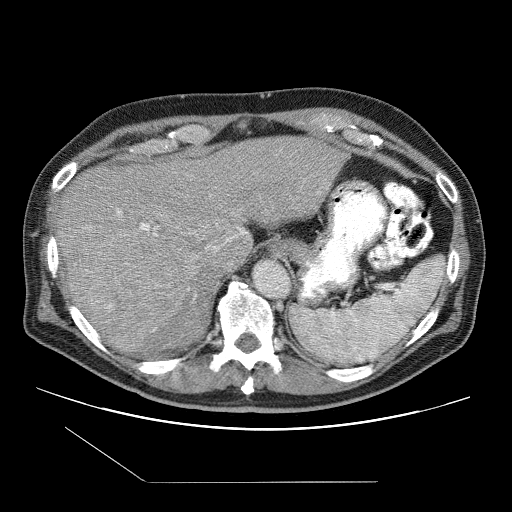
Contrast-enhanced abdominal CT (liver protocol), one axial slice; position 76 of 109 along the scan axis; one of 2 acquisitions stored at this slice position; soft-tissue window (W 400 / L 40 HU); 2.5 mm slice thickness; 512 × 512 image matrix, field of view 400 × 400 mm. From the clinical record (not read from this slice): diagnosis: hepatocellular carcinoma (patient treated with transarterial chemoembolisation; whether this scan precedes or follows treatment is not stated here); TNM stage (as recorded): Stage-IIIB; Child-Pugh class: A; tumour differentiation: well differentiated; tumour nodularity: multinodular.
Outlined on this slice (semi-automatic segmentation, software-assisted and operator-edited):
- liver parenchyma outside the tumour (the mass and vessels are separate outlines, so this box may not span the whole liver): bounding box (x1, y1, x2, y2) in pixels: (56, 136, 344, 350)
- mass: (68, 222, 192, 355)
- liver vessels: (118, 210, 245, 249)